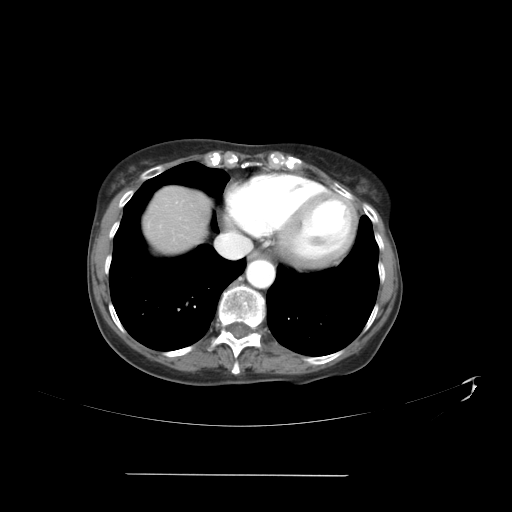
Contrast-enhanced abdominal CT, one axial slice. Position 37 of 41 along the scan axis. Reconstruction kernel STANDARD. Intravenous contrast given. Soft-tissue window (W 400 / L 40 HU). 5 mm slice thickness. 512 × 512 image matrix, field of view 431 × 431 mm. Female patient, age 74 years. From the clinical record (not read from this slice): diagnosis: colorectal cancer liver metastases, imaged before liver resection; multiple liver metastases: yes; largest metastasis: 3.3 cm; disease in both lobes: yes.
Outlined on this slice (expert manual segmentation):
- liver: bounding box [x1, y1, x2, y2] px = [146, 188, 208, 251]
- planned liver remnant (the part of the liver to remain after resection): [146, 188, 208, 246]